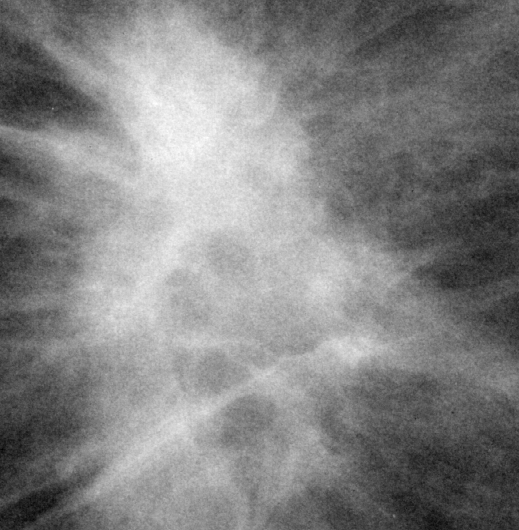
Cropped region of a digitized screen-film mammogram centred on a radiologist-marked abnormality; right breast; CC view; BI-RADS breast density category 2 (scale 1–4).
- Marked abnormality: mass, shape irregular / architectural distortion, margins spiculated; BI-RADS assessment category 5; pathology (as recorded): malignant.